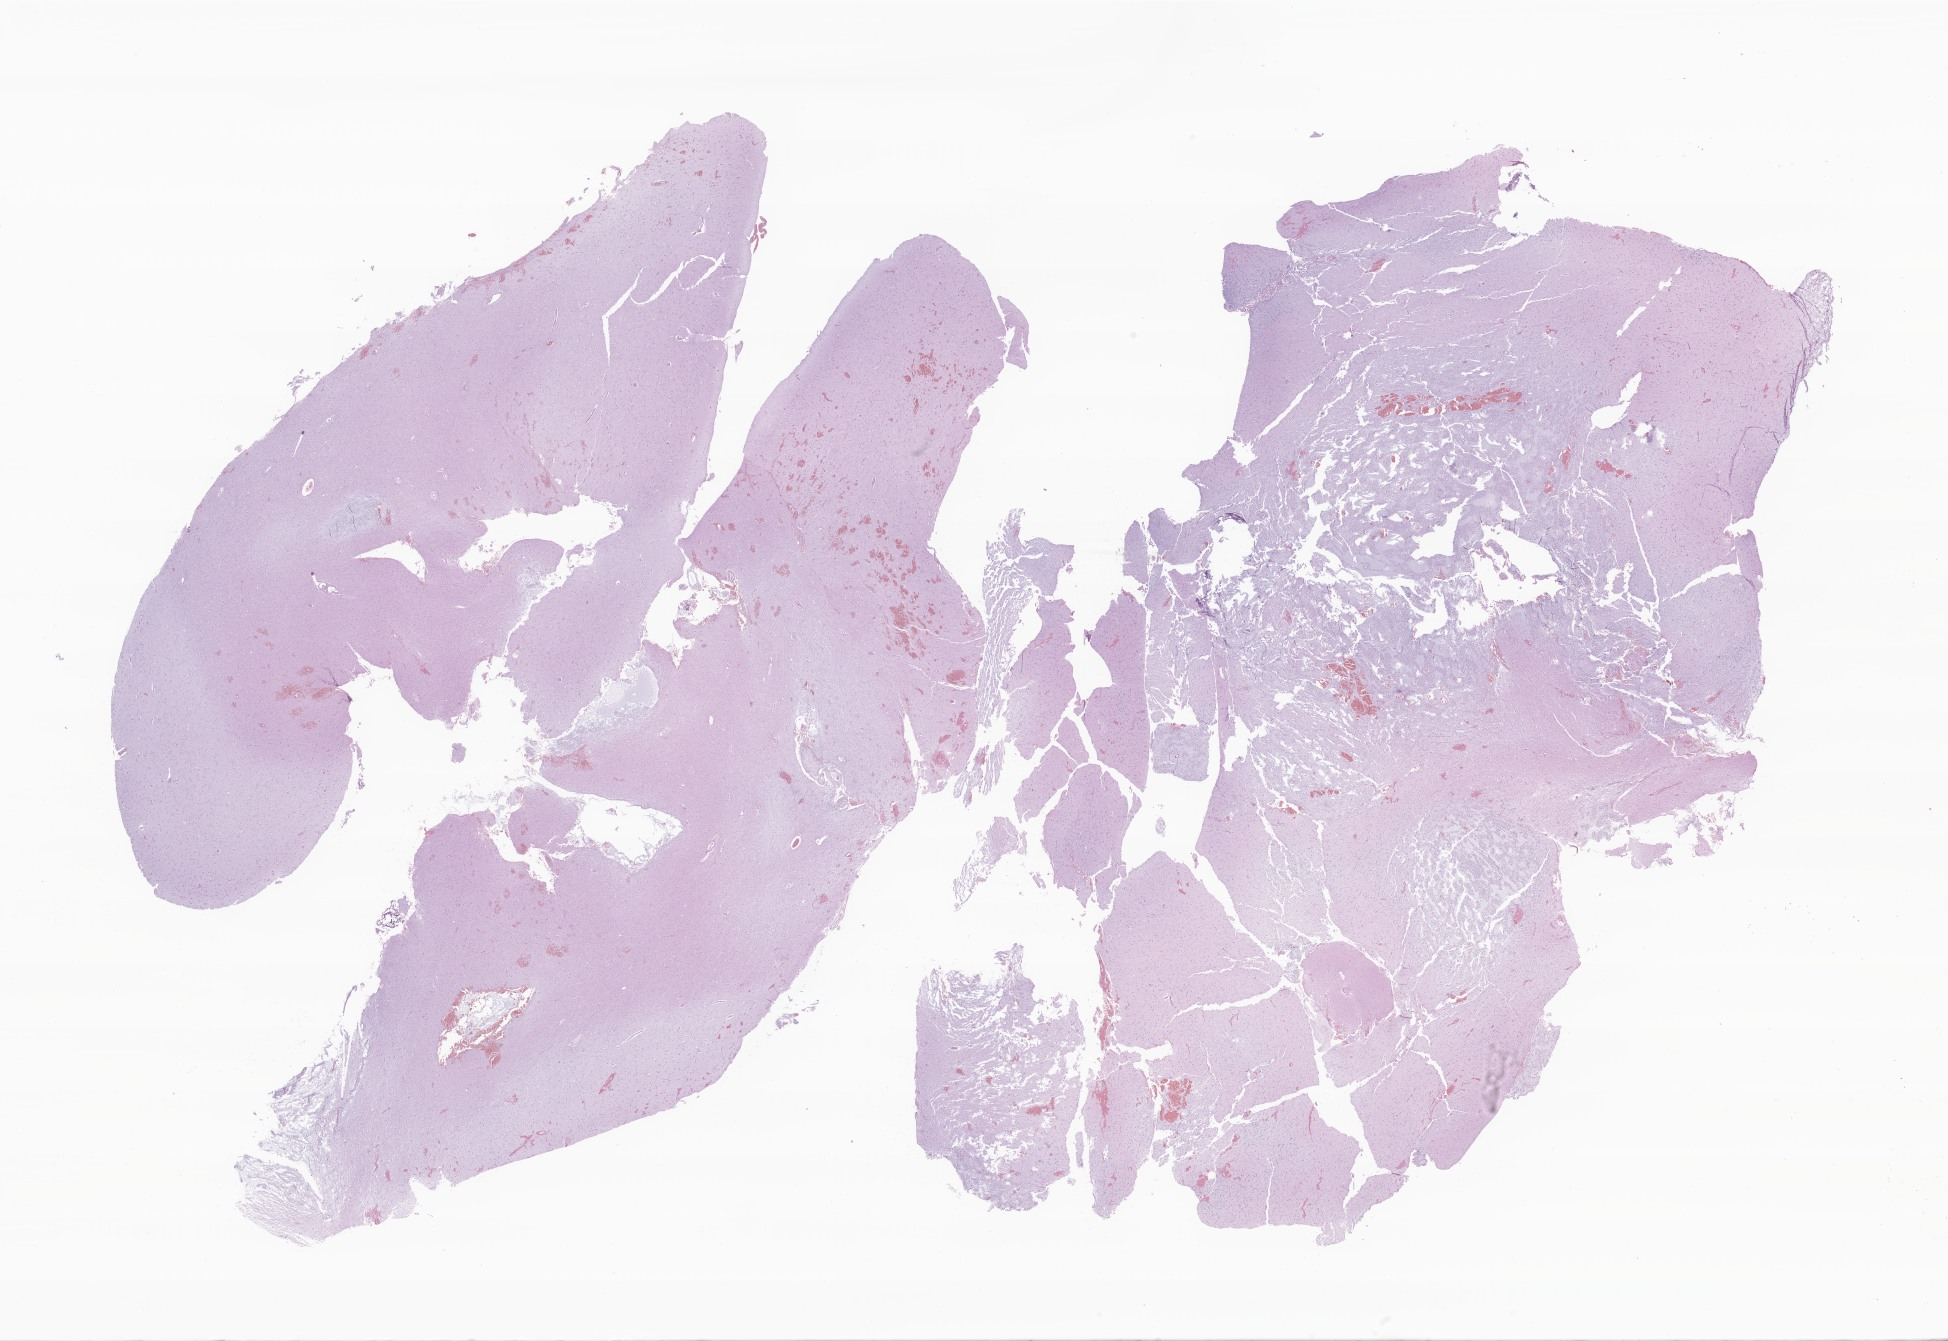
Digitized H&E-stained section of tumor tissue from the brain — a low-resolution overview of the entire scanned area, about 32.9 x 22.6 mm, formalin-fixed paraffin-embedded section. Patient male; age 127 months (10 years 7 months).
- diagnosis: Dysembryoplastic neuroepithelial tumor